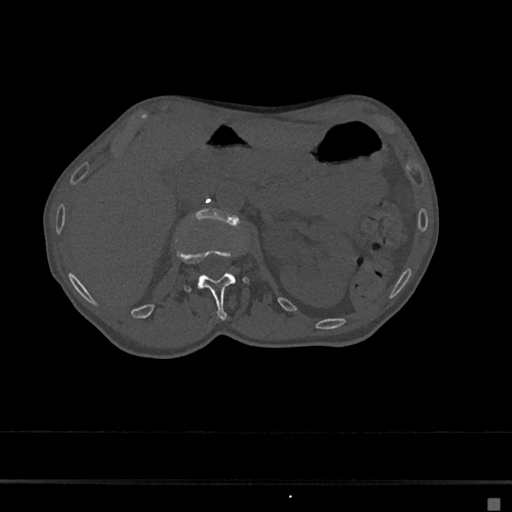
CT including the spine, one axial slice. Position 60 of 797 along the scan axis. Bone window (W 1800 / L 400 HU). 0.5 mm slice thickness. 512 × 512 image matrix, field of view 360 × 360 mm. Patient: female, 68 years. From the clinical record (not read from this slice): primary cancer: renal.
Outlined on this slice (semi-automatically segmented with operator editing):
- L1 vertebra: box from (x=176, y=247) to (x=250, y=319) px
- L2 vertebra: (x=199, y=209)–(x=238, y=223)